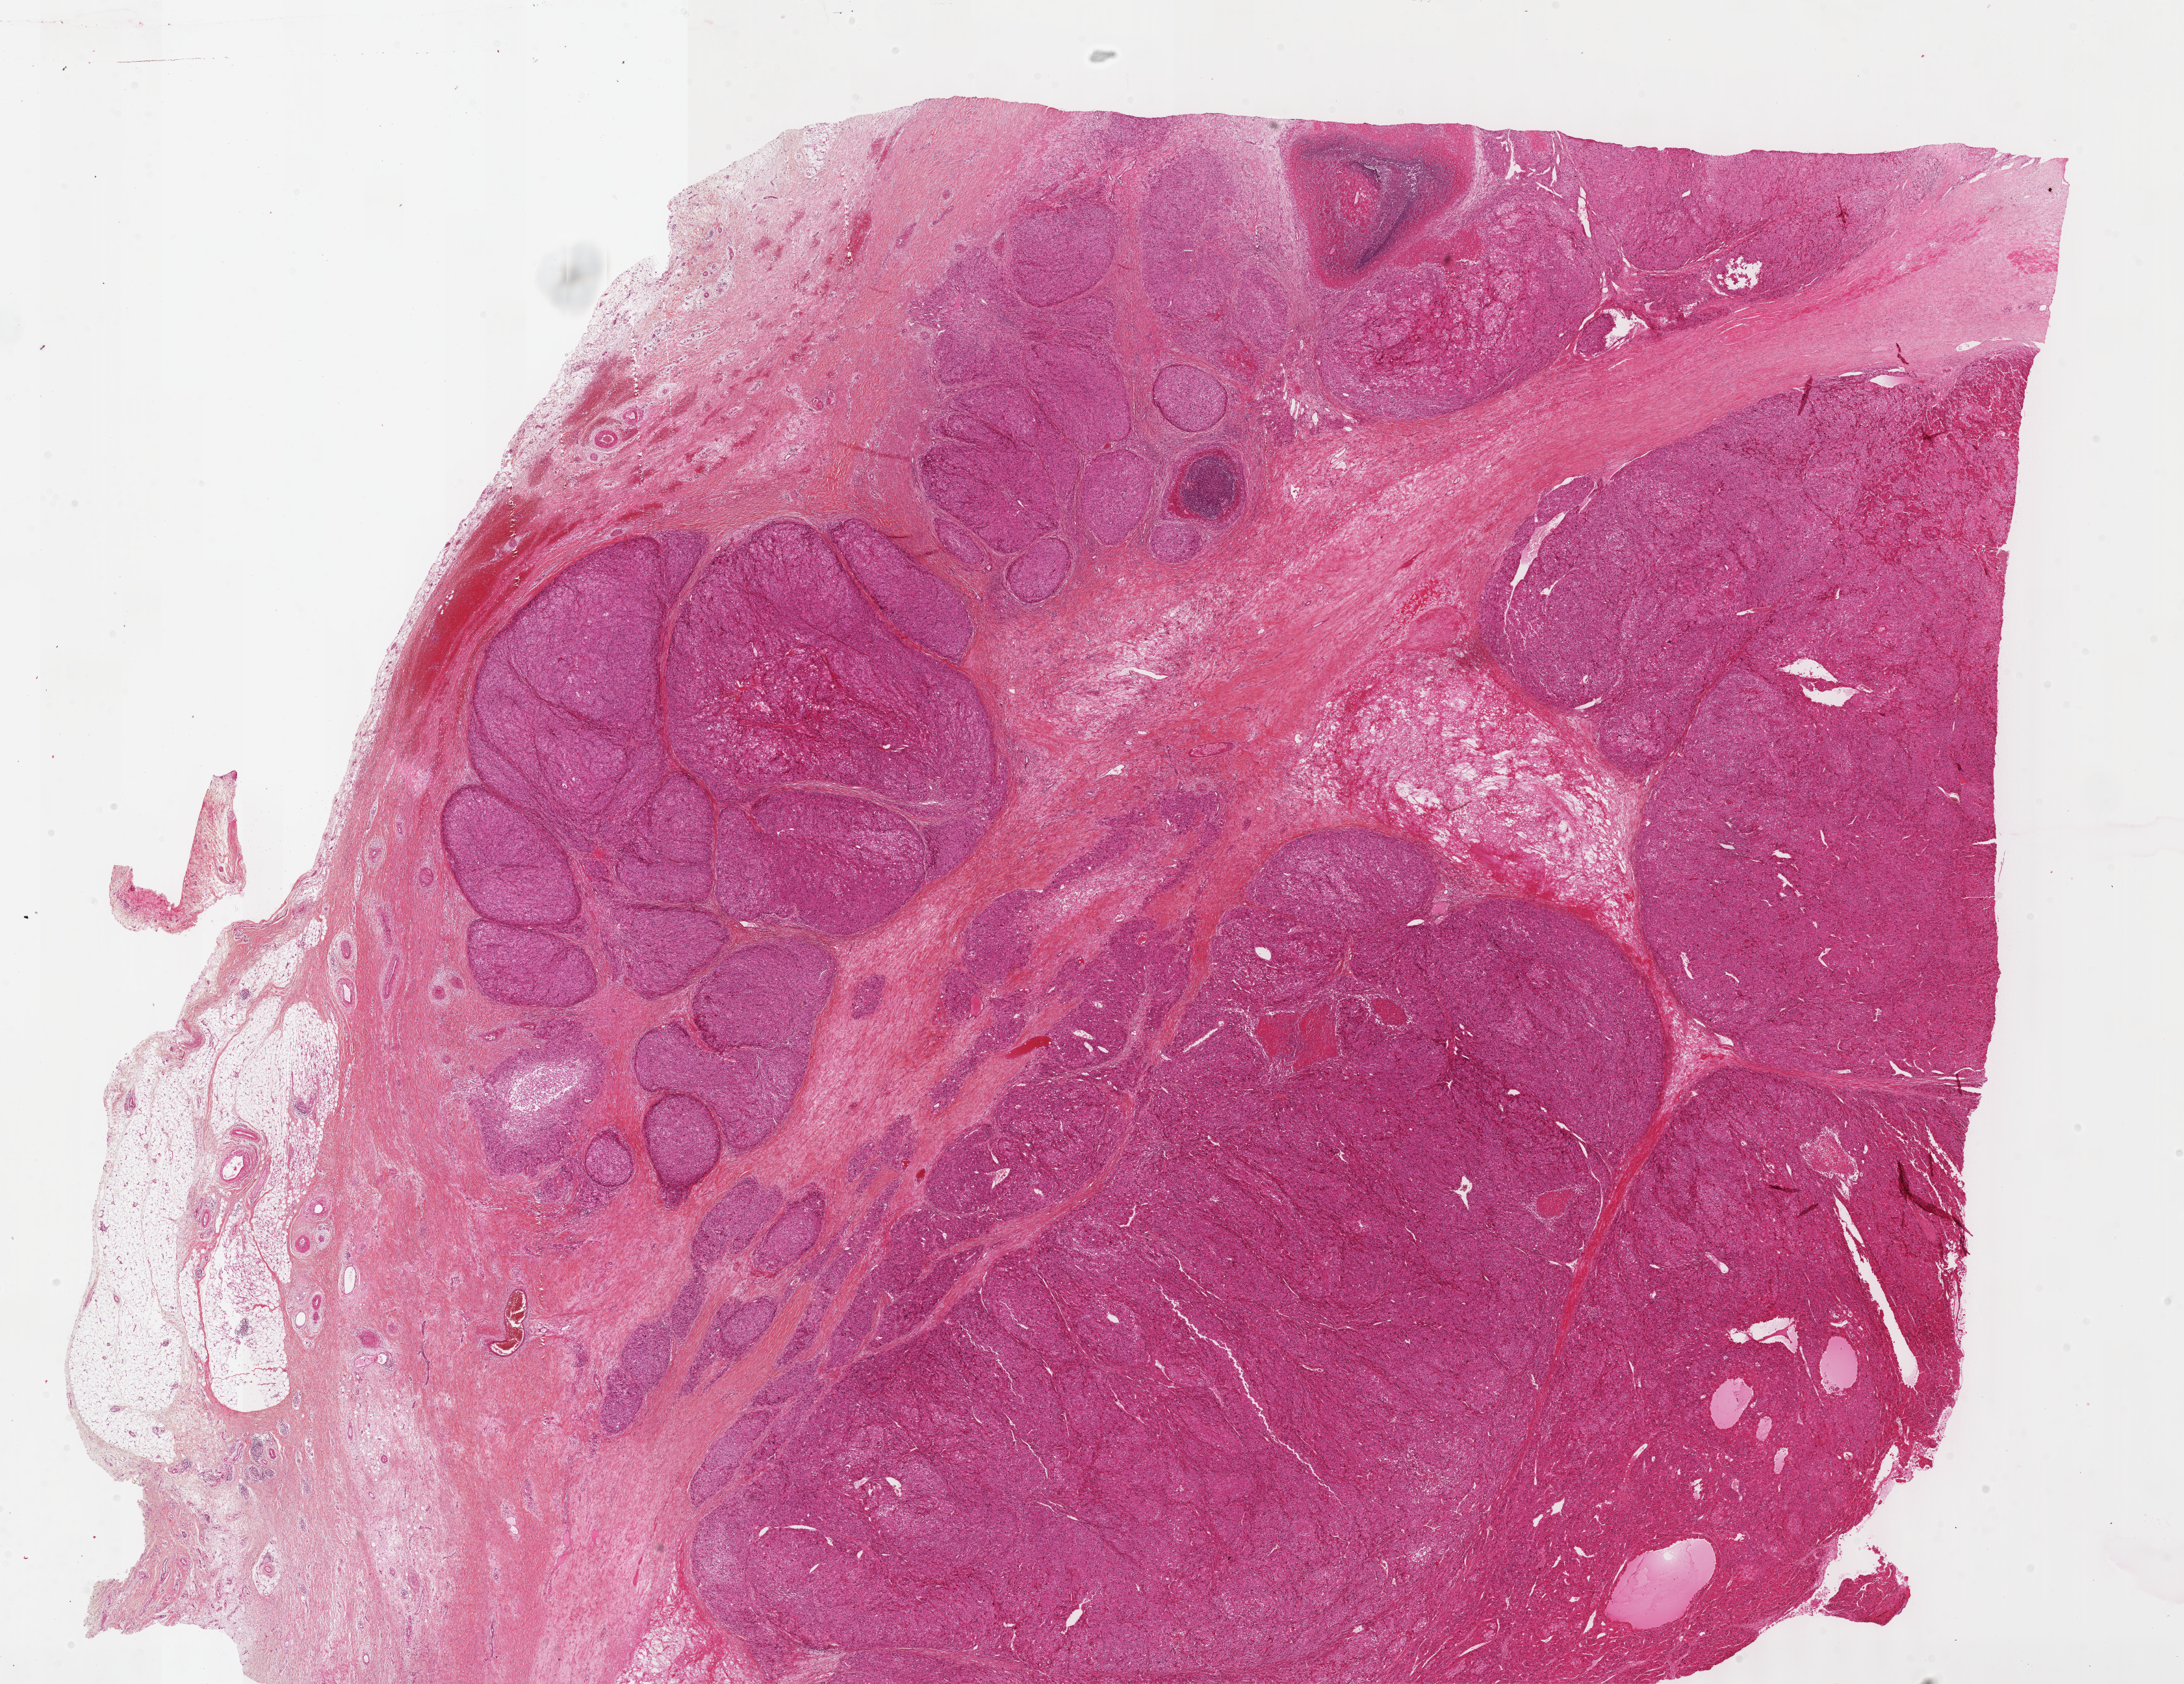
Digitized Hematoxylin and eosin (H&E) stained tissue section (whole slide) — shown as a low-resolution overview of the whole scanned area (about 27.2 x 20.9 mm). Formalin-fixed paraffin-embedded (FFPE) diagnostic section. Primary tumour sample from the adrenal cortex. Male, age 23 years at initial diagnosis.
- laterality: right
- diagnosis: Adrenal cortical carcinoma (cortex of adrenal gland)
- lymph nodes positive (case pathology): 0 of 32 examined